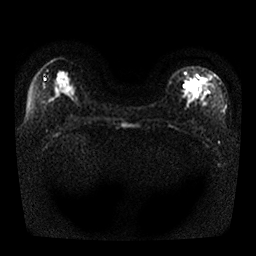
Breast MRI, one axial slice; position 14 of 25 along the scan axis; diffusion-weighted series; image 2 of 4 stored at this slice position (different b-values; order by instance number); 1.5 T; 4 mm slice thickness; 256 × 256 image matrix, field of view 330 × 330 mm. Female patient.
Annotated regions visible in this slice (expert manual segmentation):
- tumour on diffusion-weighted imaging: bounding box <186,76,205,92> (left, top, right, bottom; pixels)